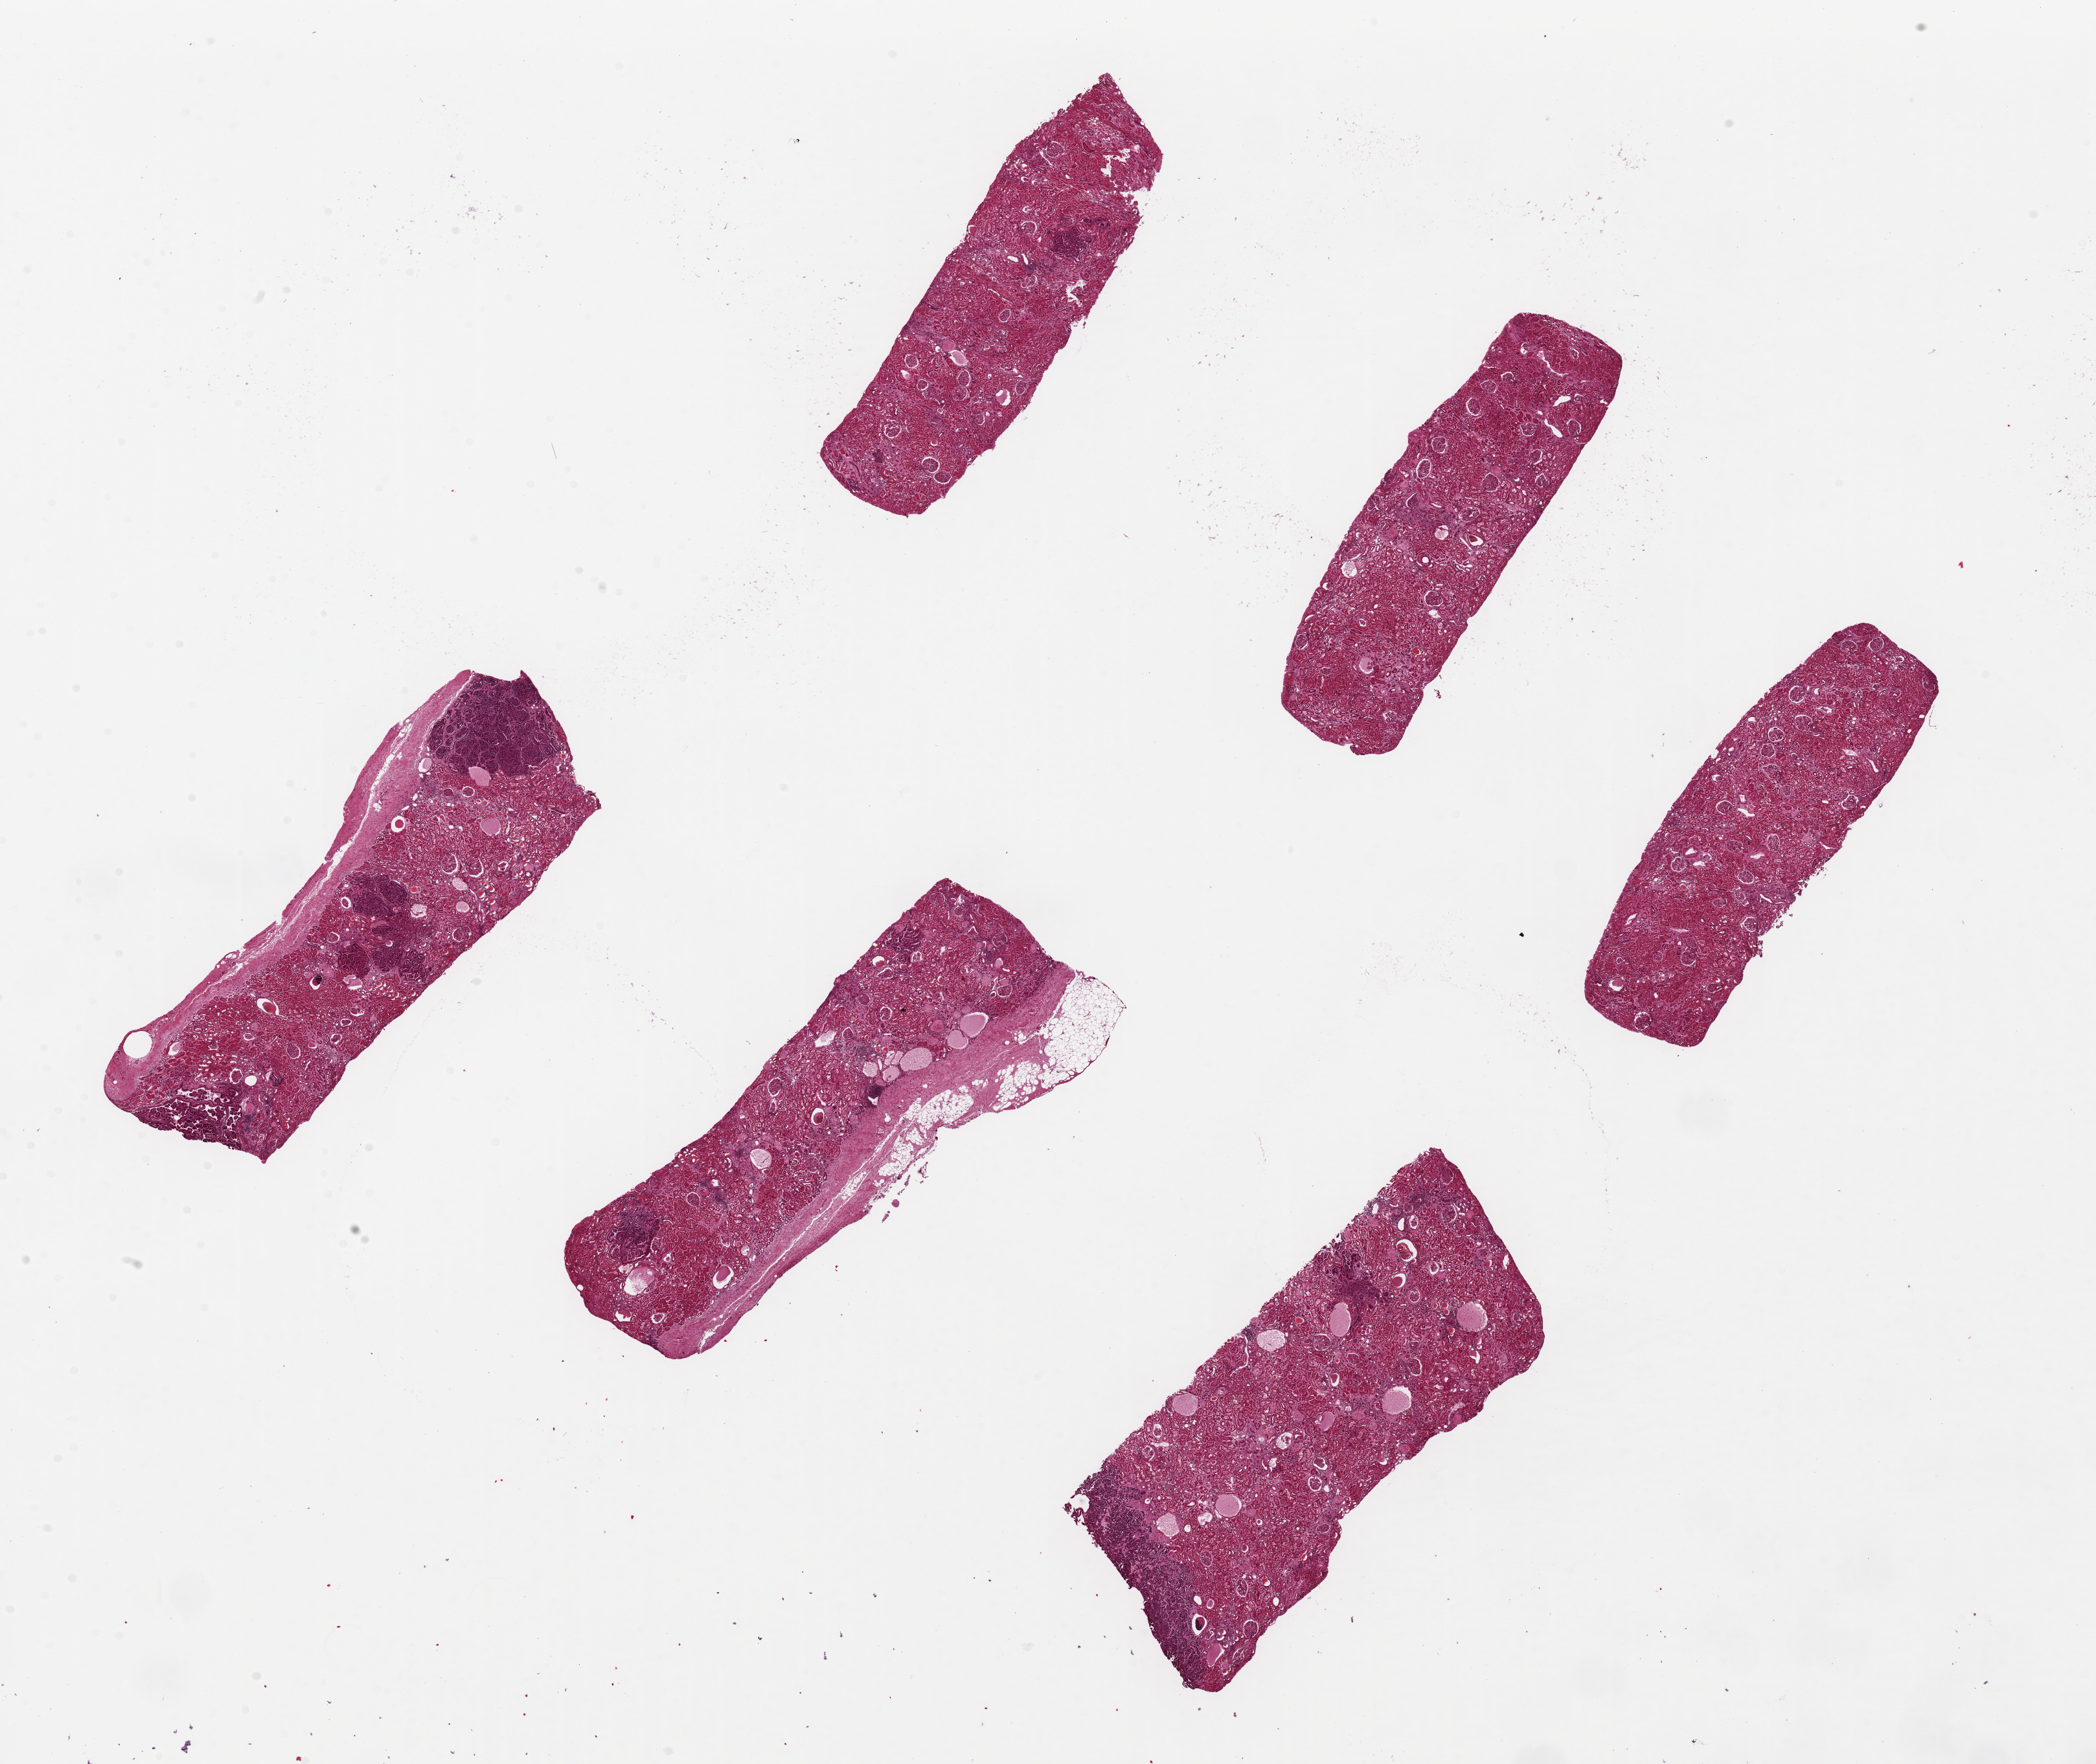
Hematoxylin and eosin (H&E) whole-slide image, brightfield, low-resolution overview of the scanned area, about 25.6 x 21.5 mm. Donor sex: male.
Specimen: PAXgene-fixed paraffin-embedded (PFPE) section; sampled site (target tissue): renal cortex; tissue donor sample.